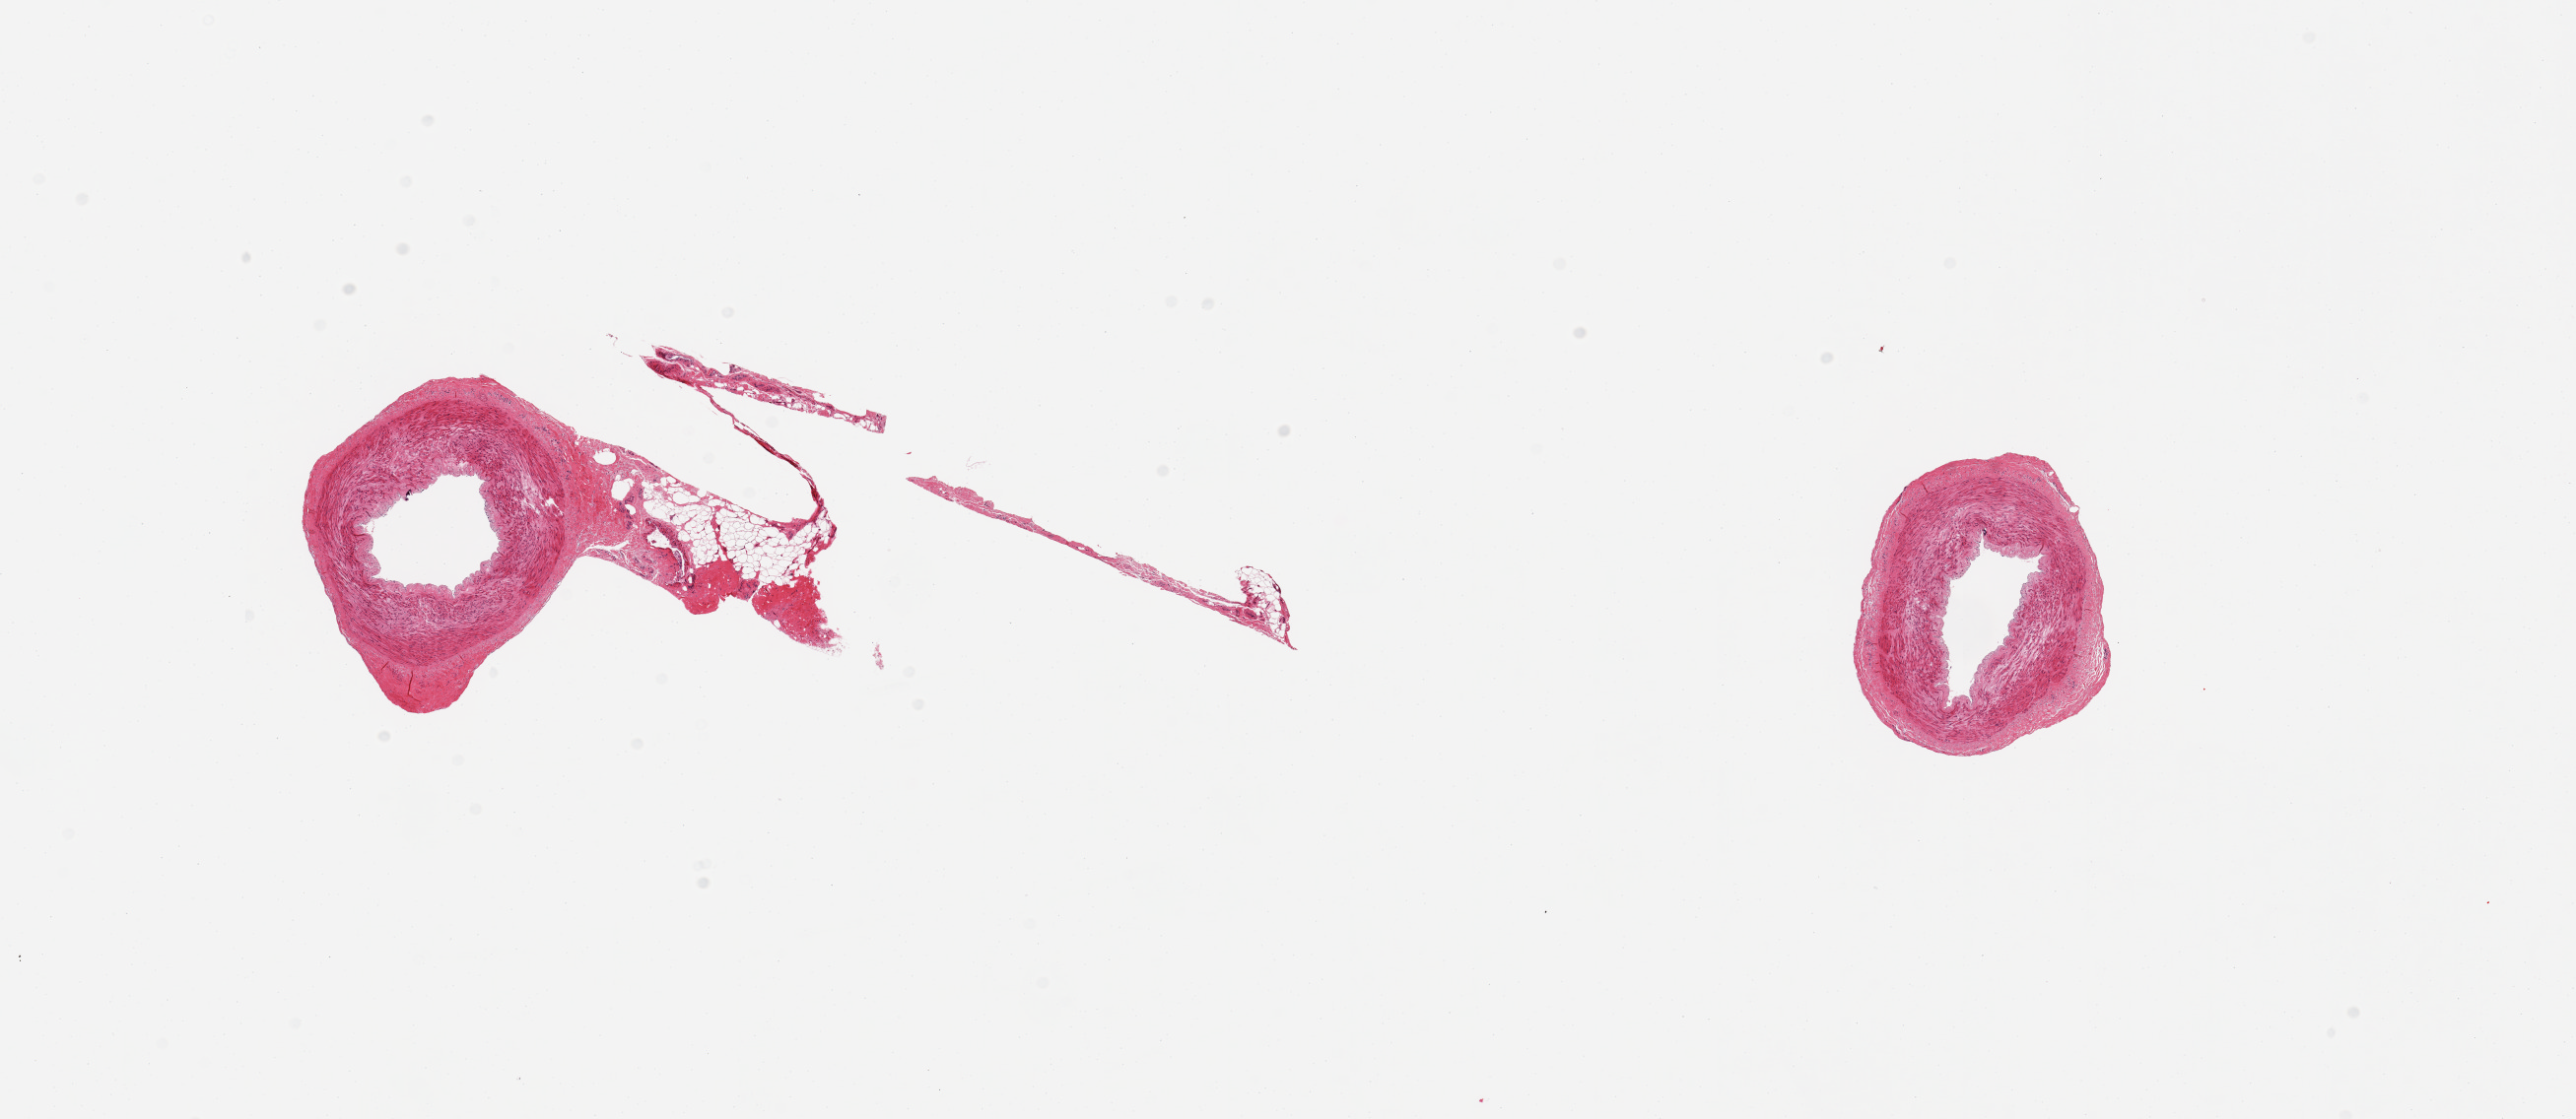
Hematoxylin and eosin (H&E) whole-slide image — a low-resolution overview of the entire scanned area, about 20.7 x 9.0 mm; PAXgene-fixed paraffin-embedded (PFPE) section; target tissue: tibial artery; donor tissue sample. Donor sex: male.
Review note (as recorded): 2 pieces; one piece includes 25% attachment of fat/extraneous tissue, trivial calcification.